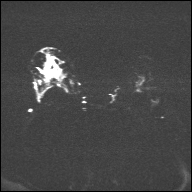
Breast MRI, one axial slice. Slice 22 of 32 in the series (ordered by position). Diffusion-weighted series; image 2 of 4 stored at this slice position (different b-values; order by instance number). 1.5 T. 192 × 192 image matrix. Female patient.
Structures marked on this image (outlined manually by an expert reader):
- tumour on diffusion-weighted imaging: bounding box <47,64,51,69> (left, top, right, bottom; pixels)